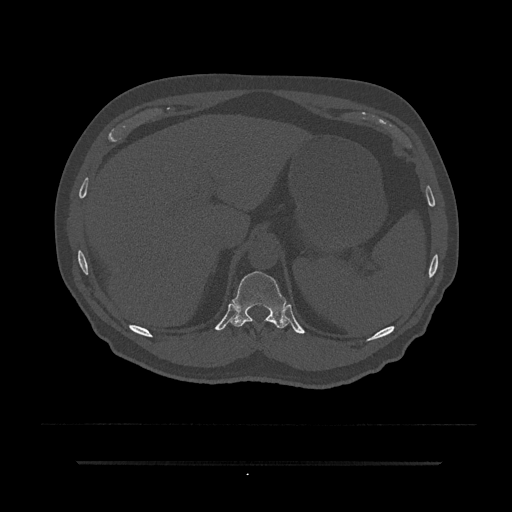
CT including the spine, one axial slice. Position 282 of 797 along the scan axis. Reconstruction kernel Br40s/3. 120 kVp. Bone window (W 1800 / L 400 HU). 0.5 mm slice thickness. 512 × 512 image matrix. Patient: male, 59 years. Case-level facts recorded for this patient, not image findings: primary cancer: bile ducts; vertebrae with lytic lesions (as recorded): T10.
Annotated regions visible in this slice (semi-automatic segmentation, software-assisted and operator-edited):
- T11 vertebra: bounding box [x1, y1, x2, y2] px = [231, 271, 291, 329]